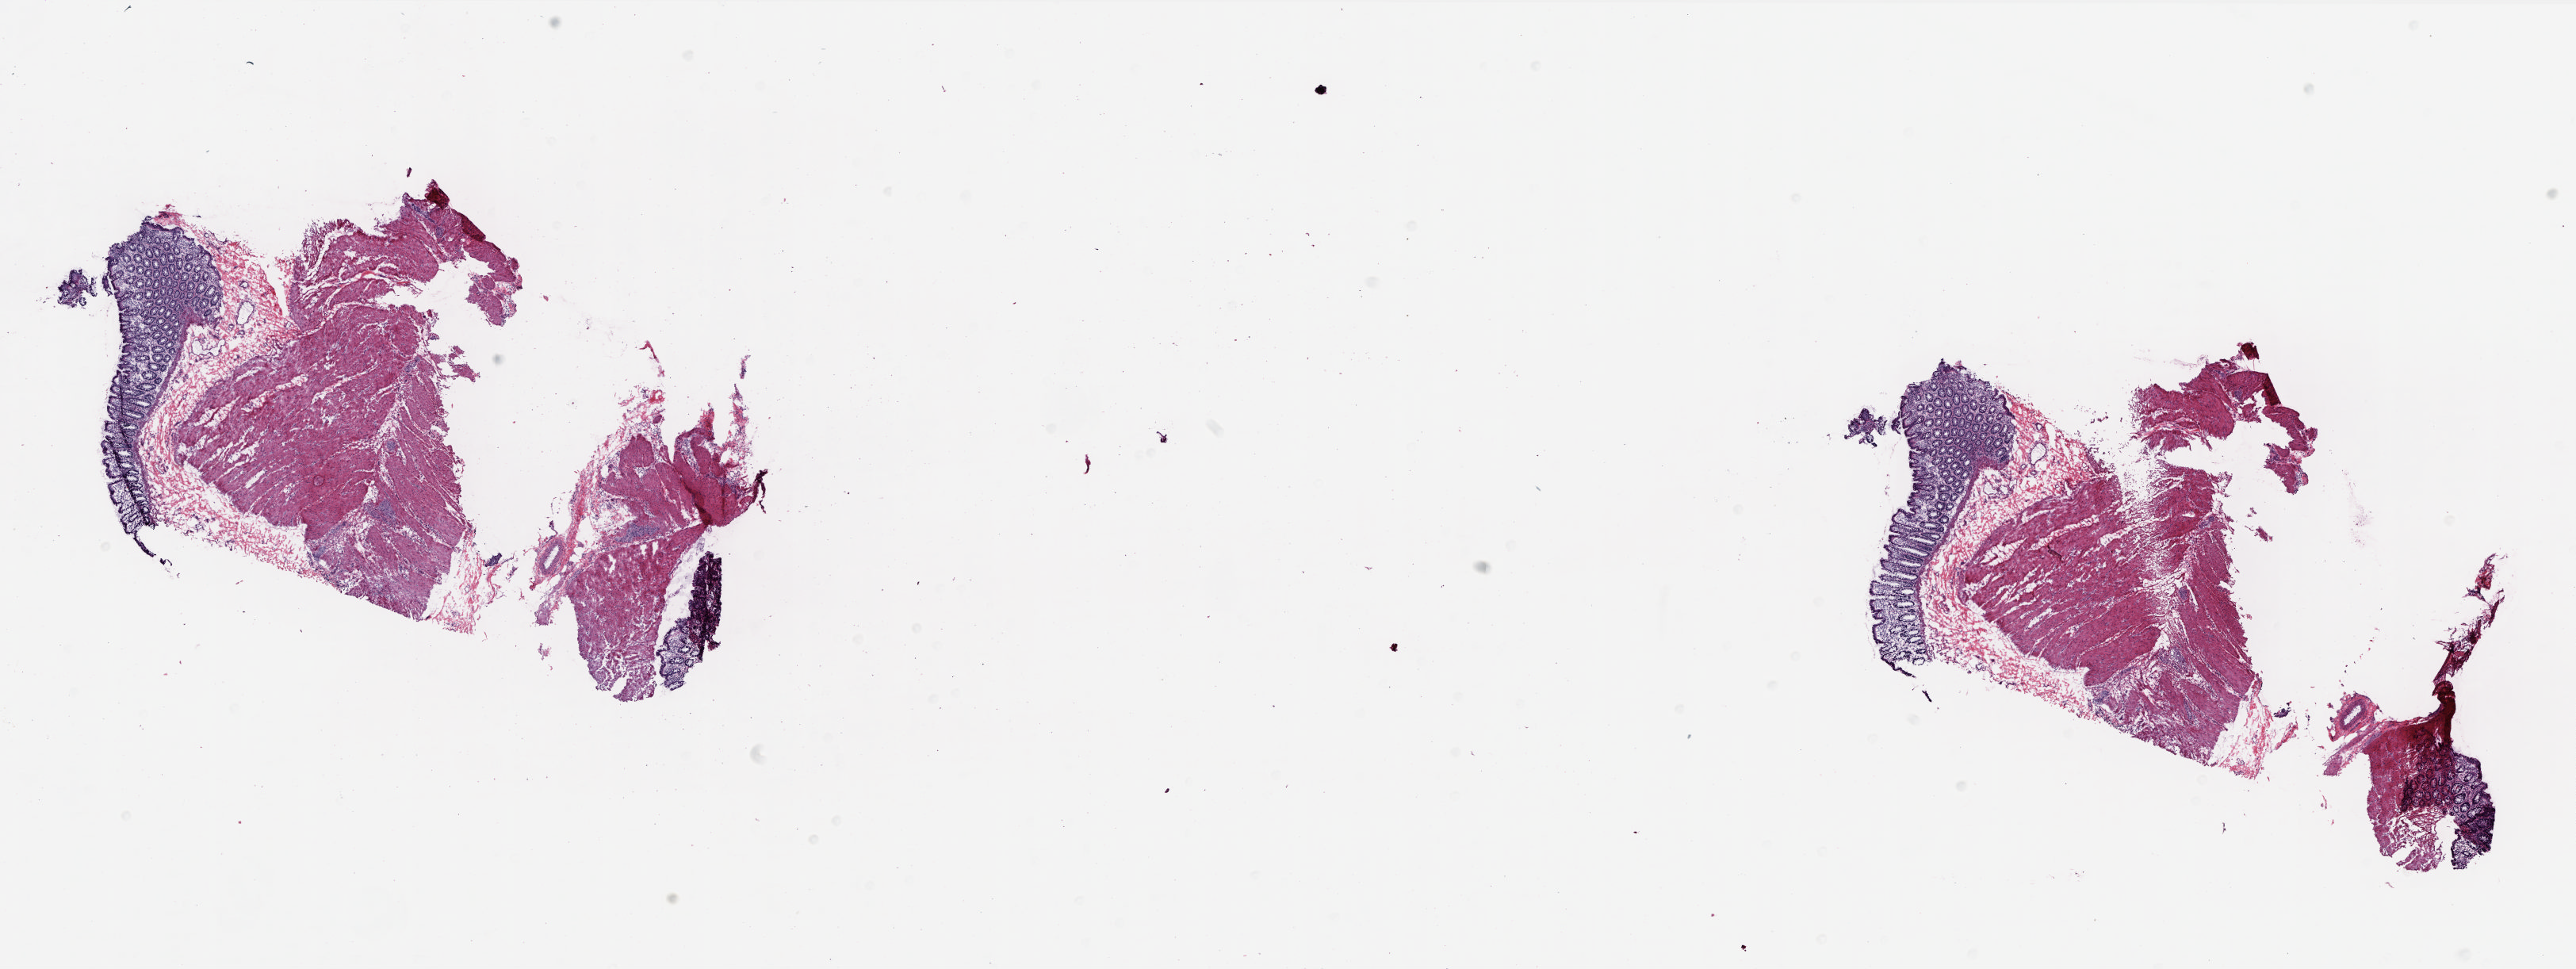
Whole-slide histology image, Hematoxylin and eosin (H&E) stained — low-resolution overview of the scanned area, about 25.9 x 9.8 mm; frozen section from the bottom of the tissue portion; solid tissue normal (non-tumour tissue) sample from the rectum. Female patient; age at initial diagnosis 57 years. Composition of this section per pathologist review: tumour cells 0%, normal cells 100%. Inflammatory infiltration, as recorded: lymphocyte infiltration 25%, monocyte infiltration 6%, neutrophil infiltration 0%.
- this section: solid tissue normal (non-tumour) sample from the same patient
- patient diagnosis: Mucinous adenocarcinoma